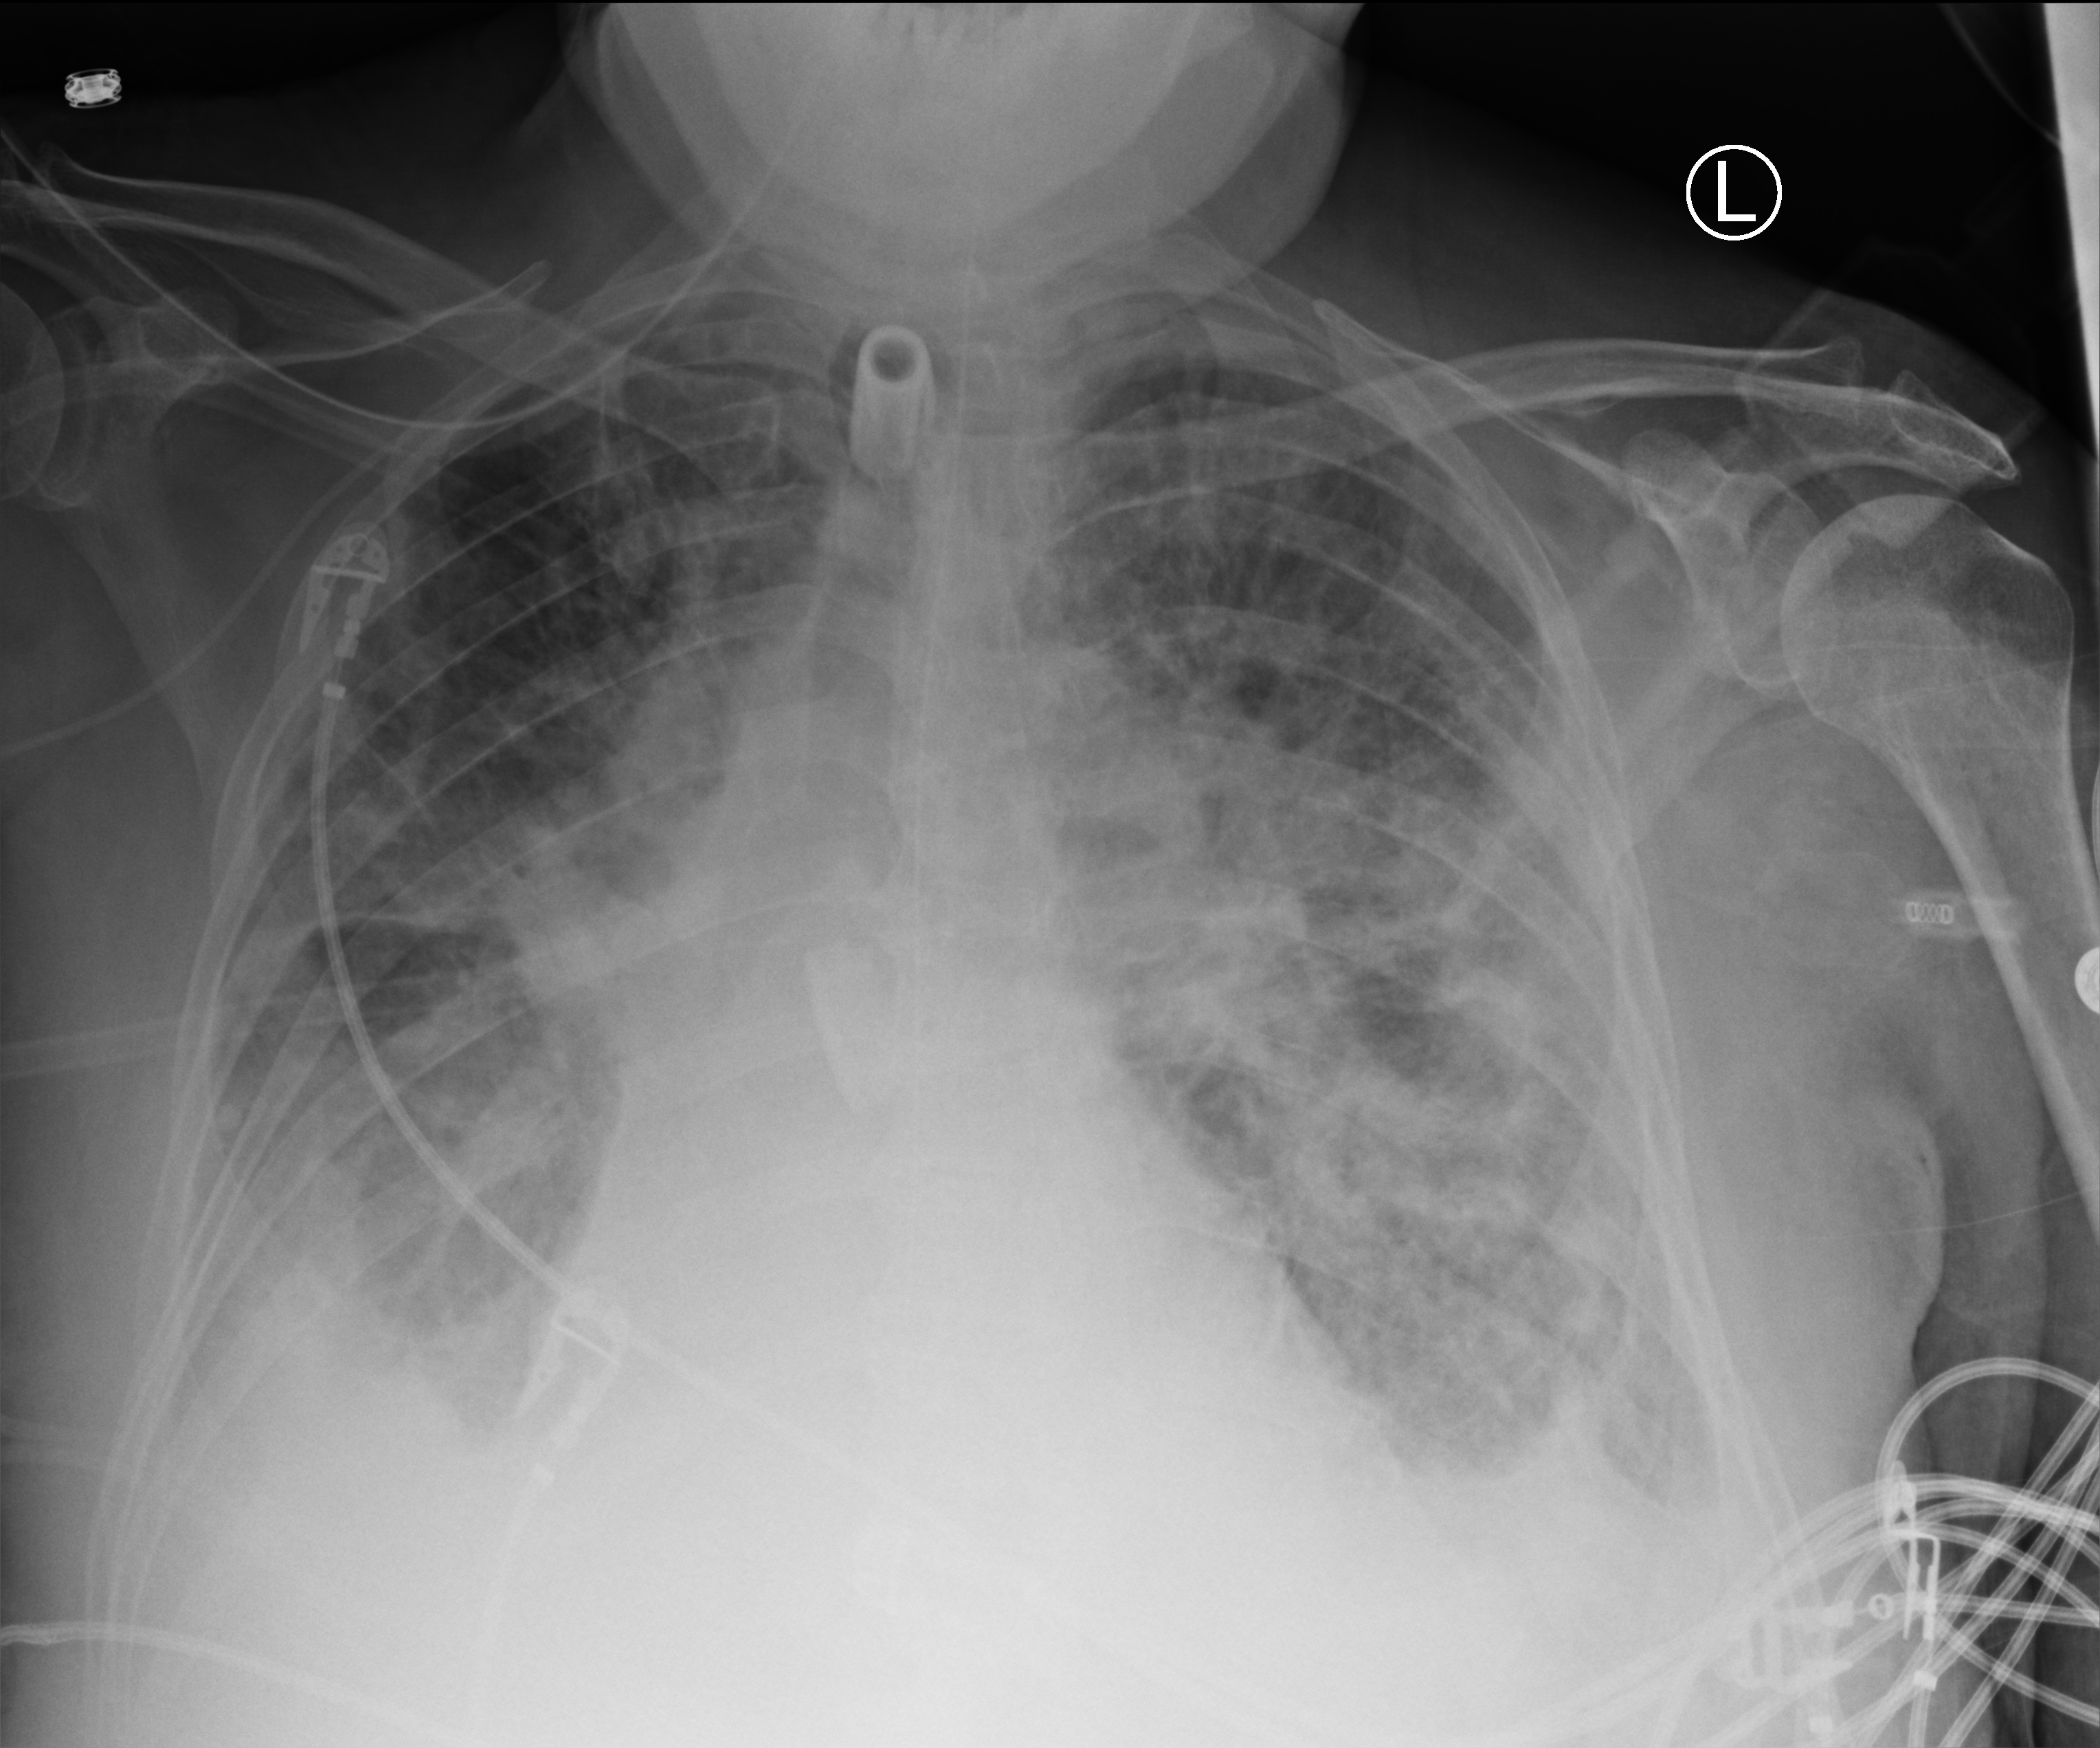
Portable chest radiograph. Patient hospitalised with COVID-19; male, aged 75–90 years.
Admission-level facts for this patient (not findings on this image; timing relative to this image not recorded): hypertension (admission record): no; admitted to intensive care during this hospital stay: yes; smoking status (admission record): never.